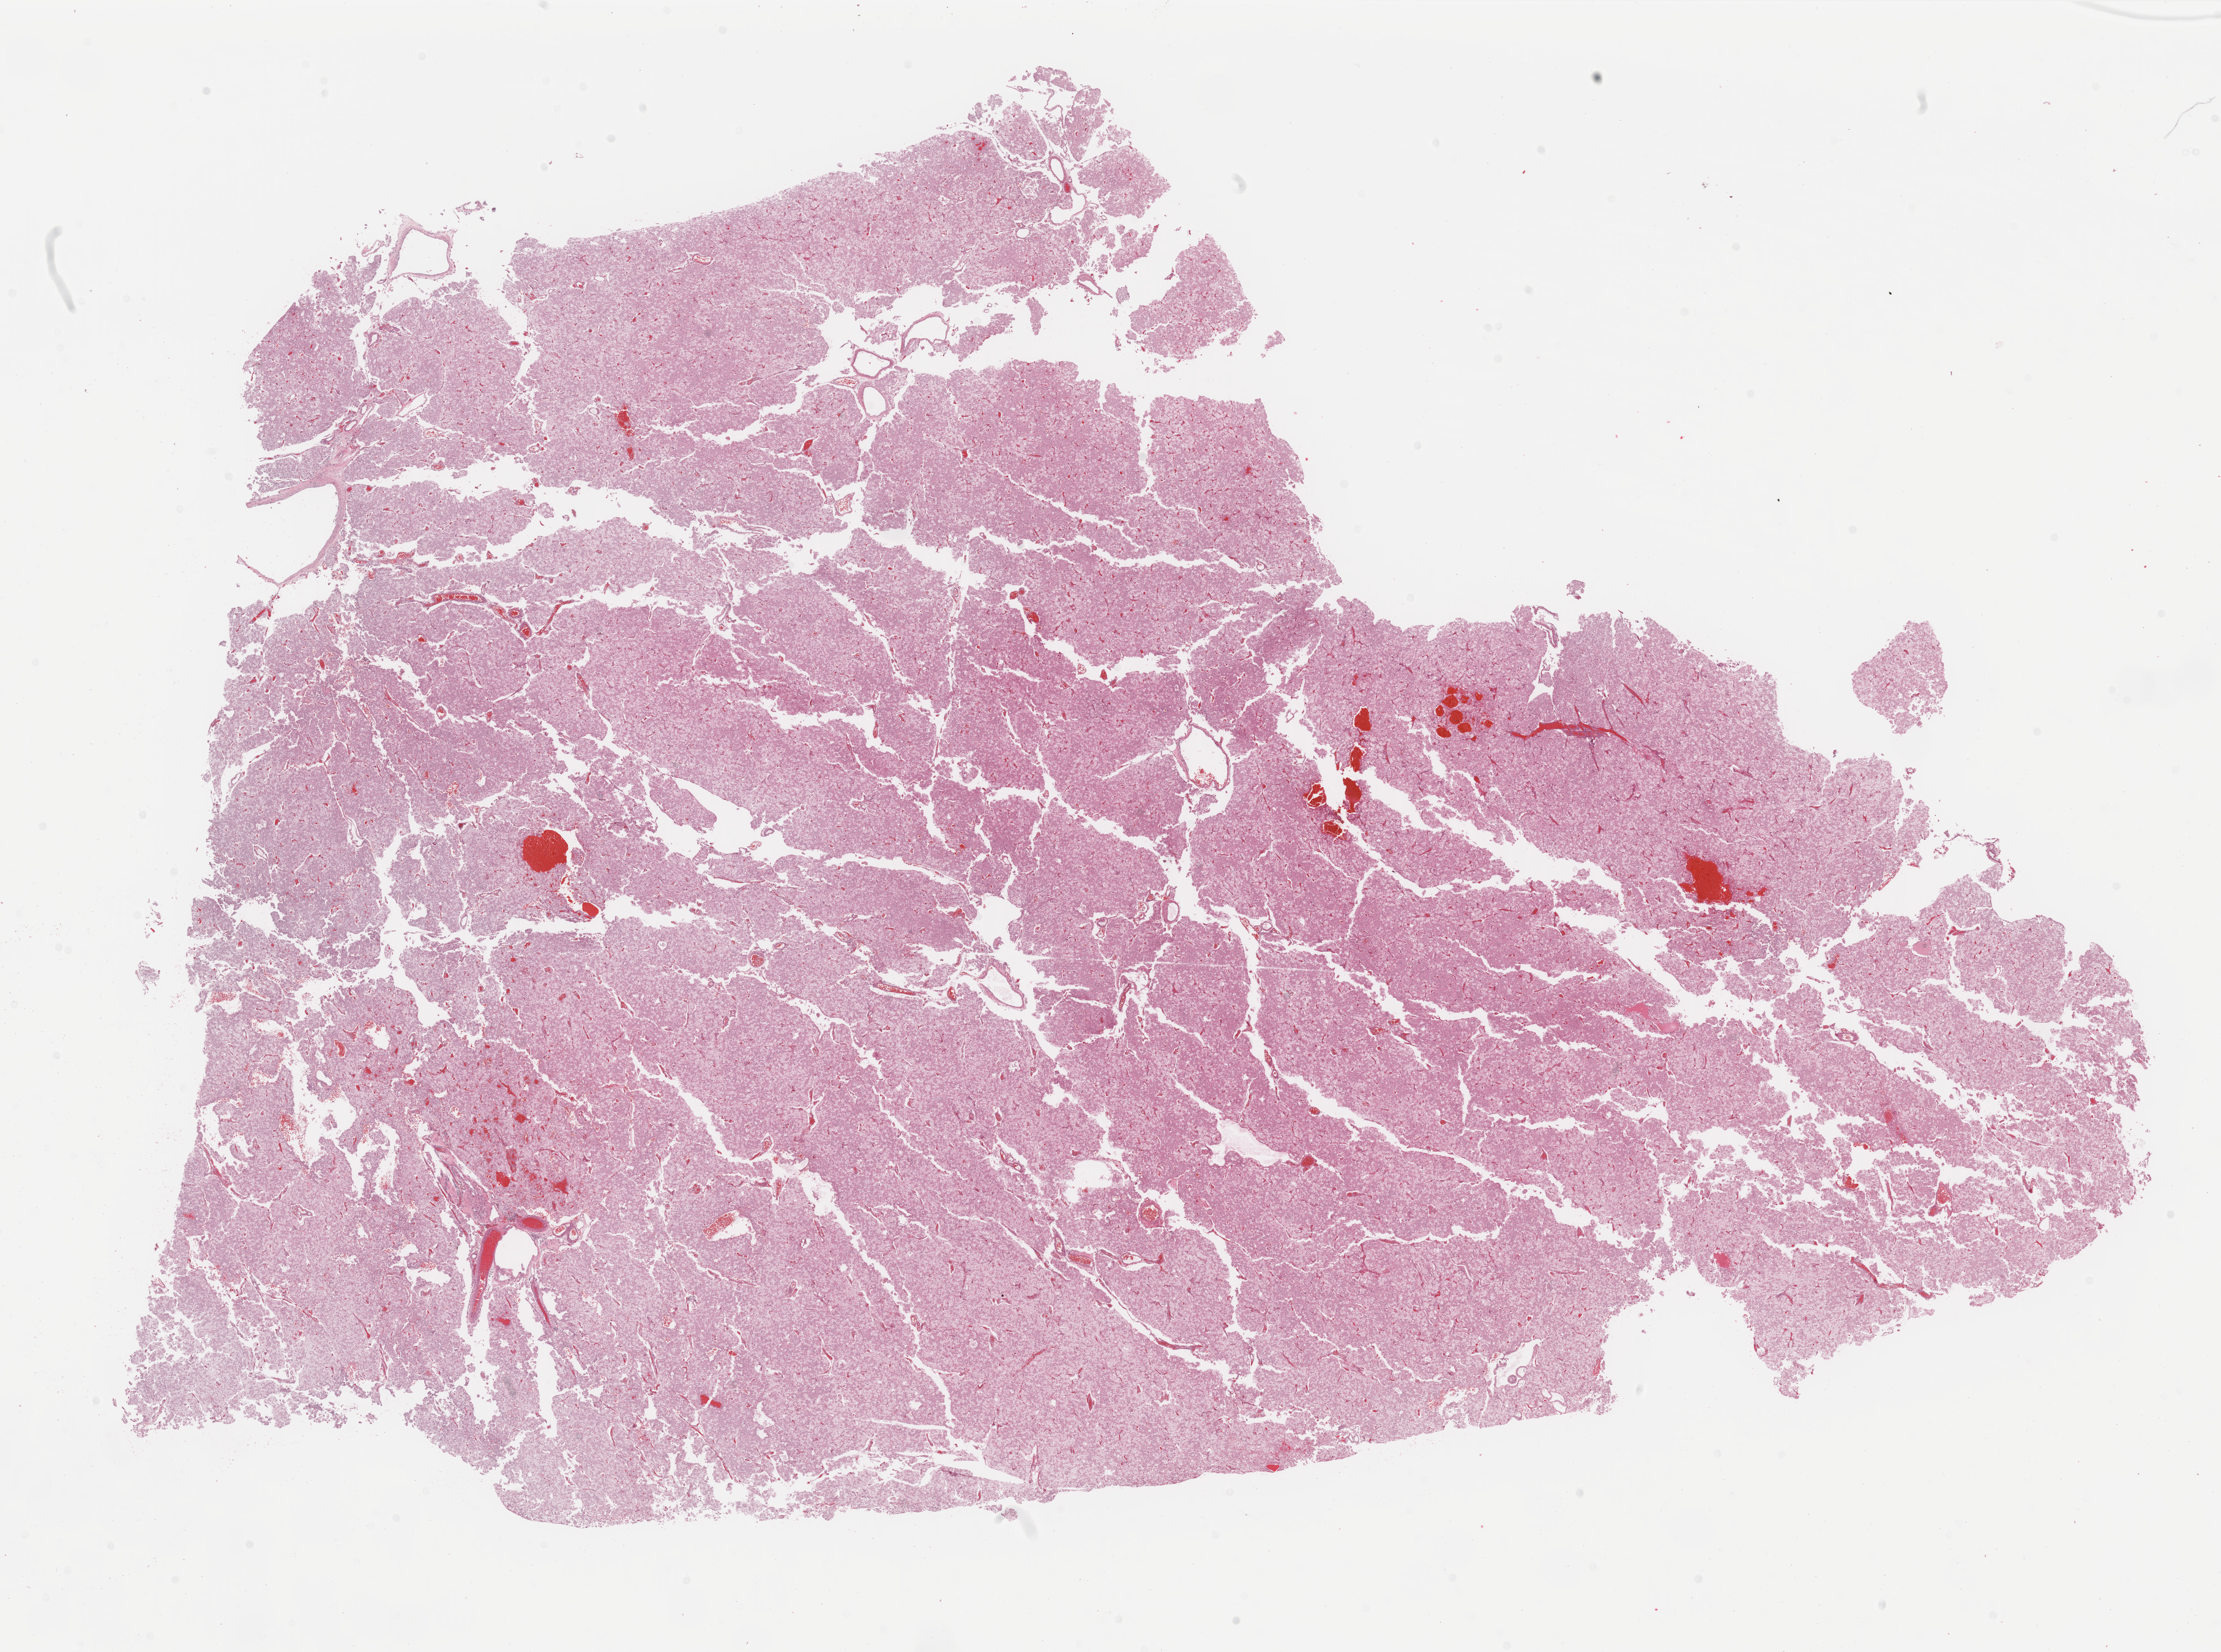
Whole-slide histology image, Hematoxylin and eosin (H&E) stained — low-resolution overview of the scanned area, about 28.7 x 21.4 mm (acquisition: 40x scan). Formalin-fixed paraffin-embedded (FFPE) diagnostic section. Kidney, primary tumour sample. Male patient; age at initial diagnosis 40 years. Composition of this section per pathologist review: tumour cells 85%, tumour nuclei 85%, normal cells 0%, stromal cells 15%, necrosis 0%. Inflammatory infiltration, as recorded: lymphocyte infiltration 0%, monocyte infiltration 0%, neutrophil infiltration 0%.
Laterality: left. Pathologic diagnosis: Renal cell carcinoma, chromophobe type. TNM: T2 NX. AJCC pathologic stage: II (6th edition).